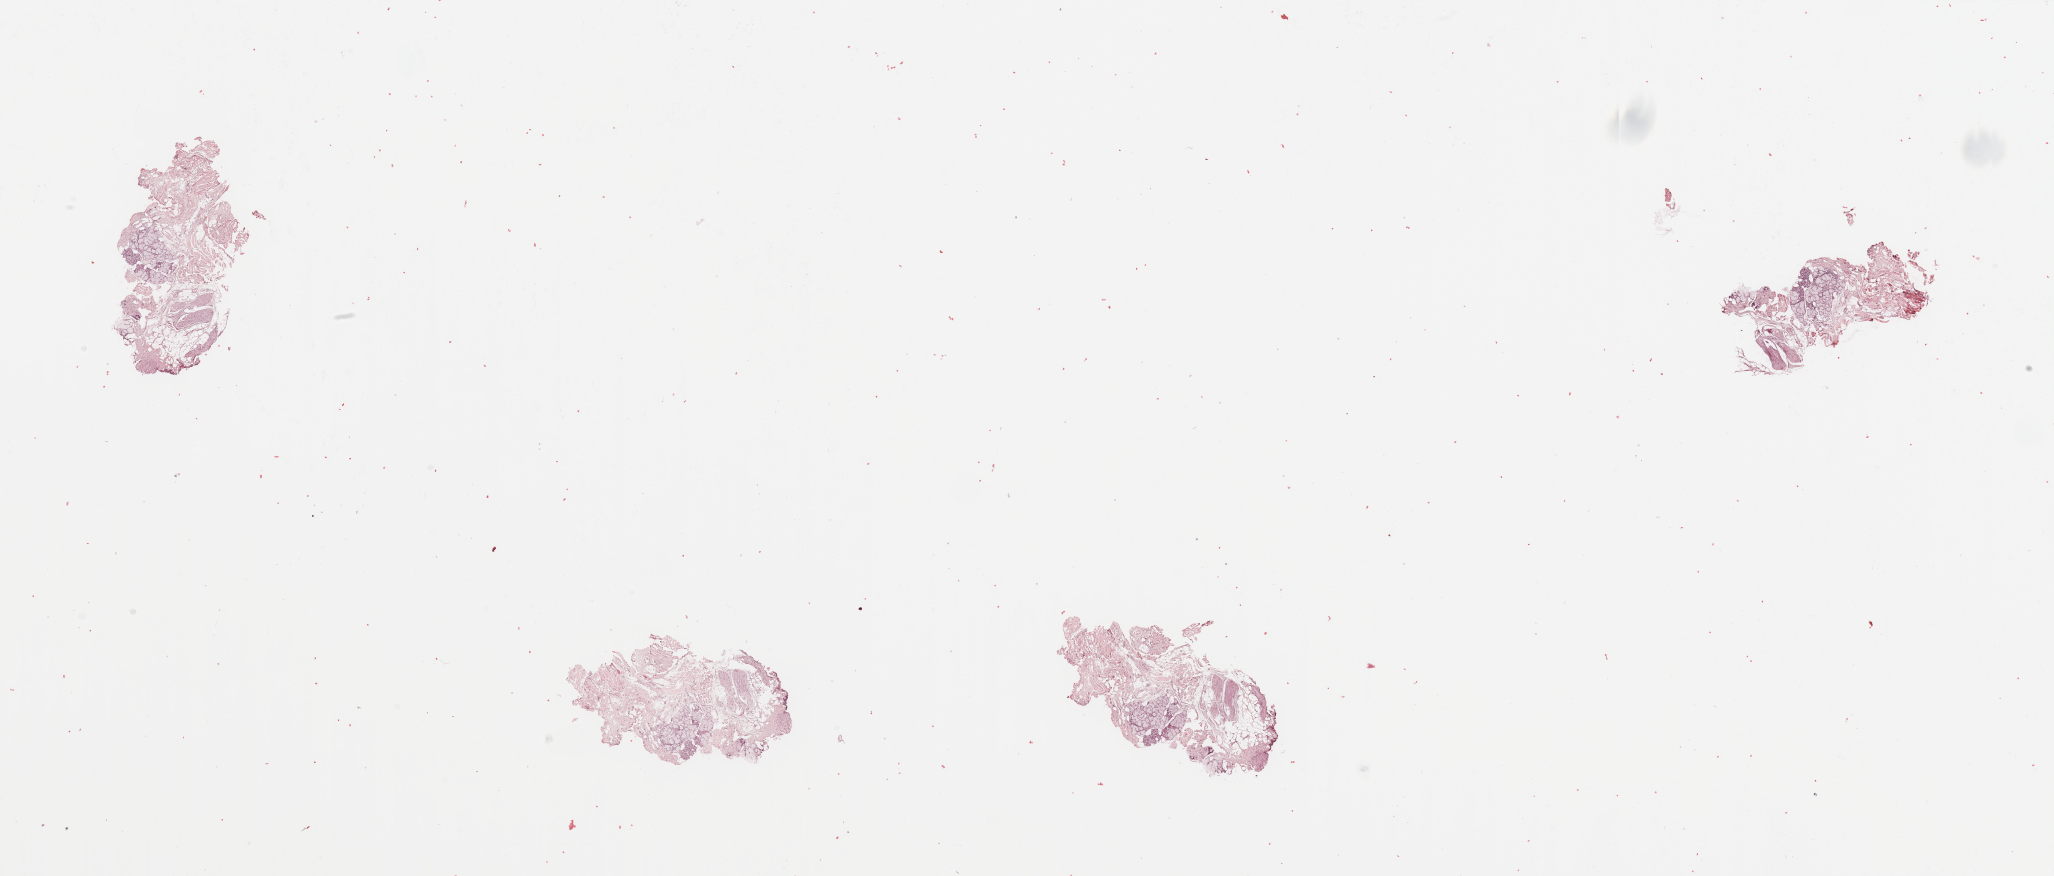
Digitized Hematoxylin and eosin (H&E) stained tissue section (whole slide), a low-resolution overview of the entire scanned area, about 32.5 x 13.9 mm (from a 20x scan). Head and neck, tissue type not recorded. Male, 66 y/o.
Patient diagnosis: Squamous cell carcinoma, NOS (tongue, NOS).